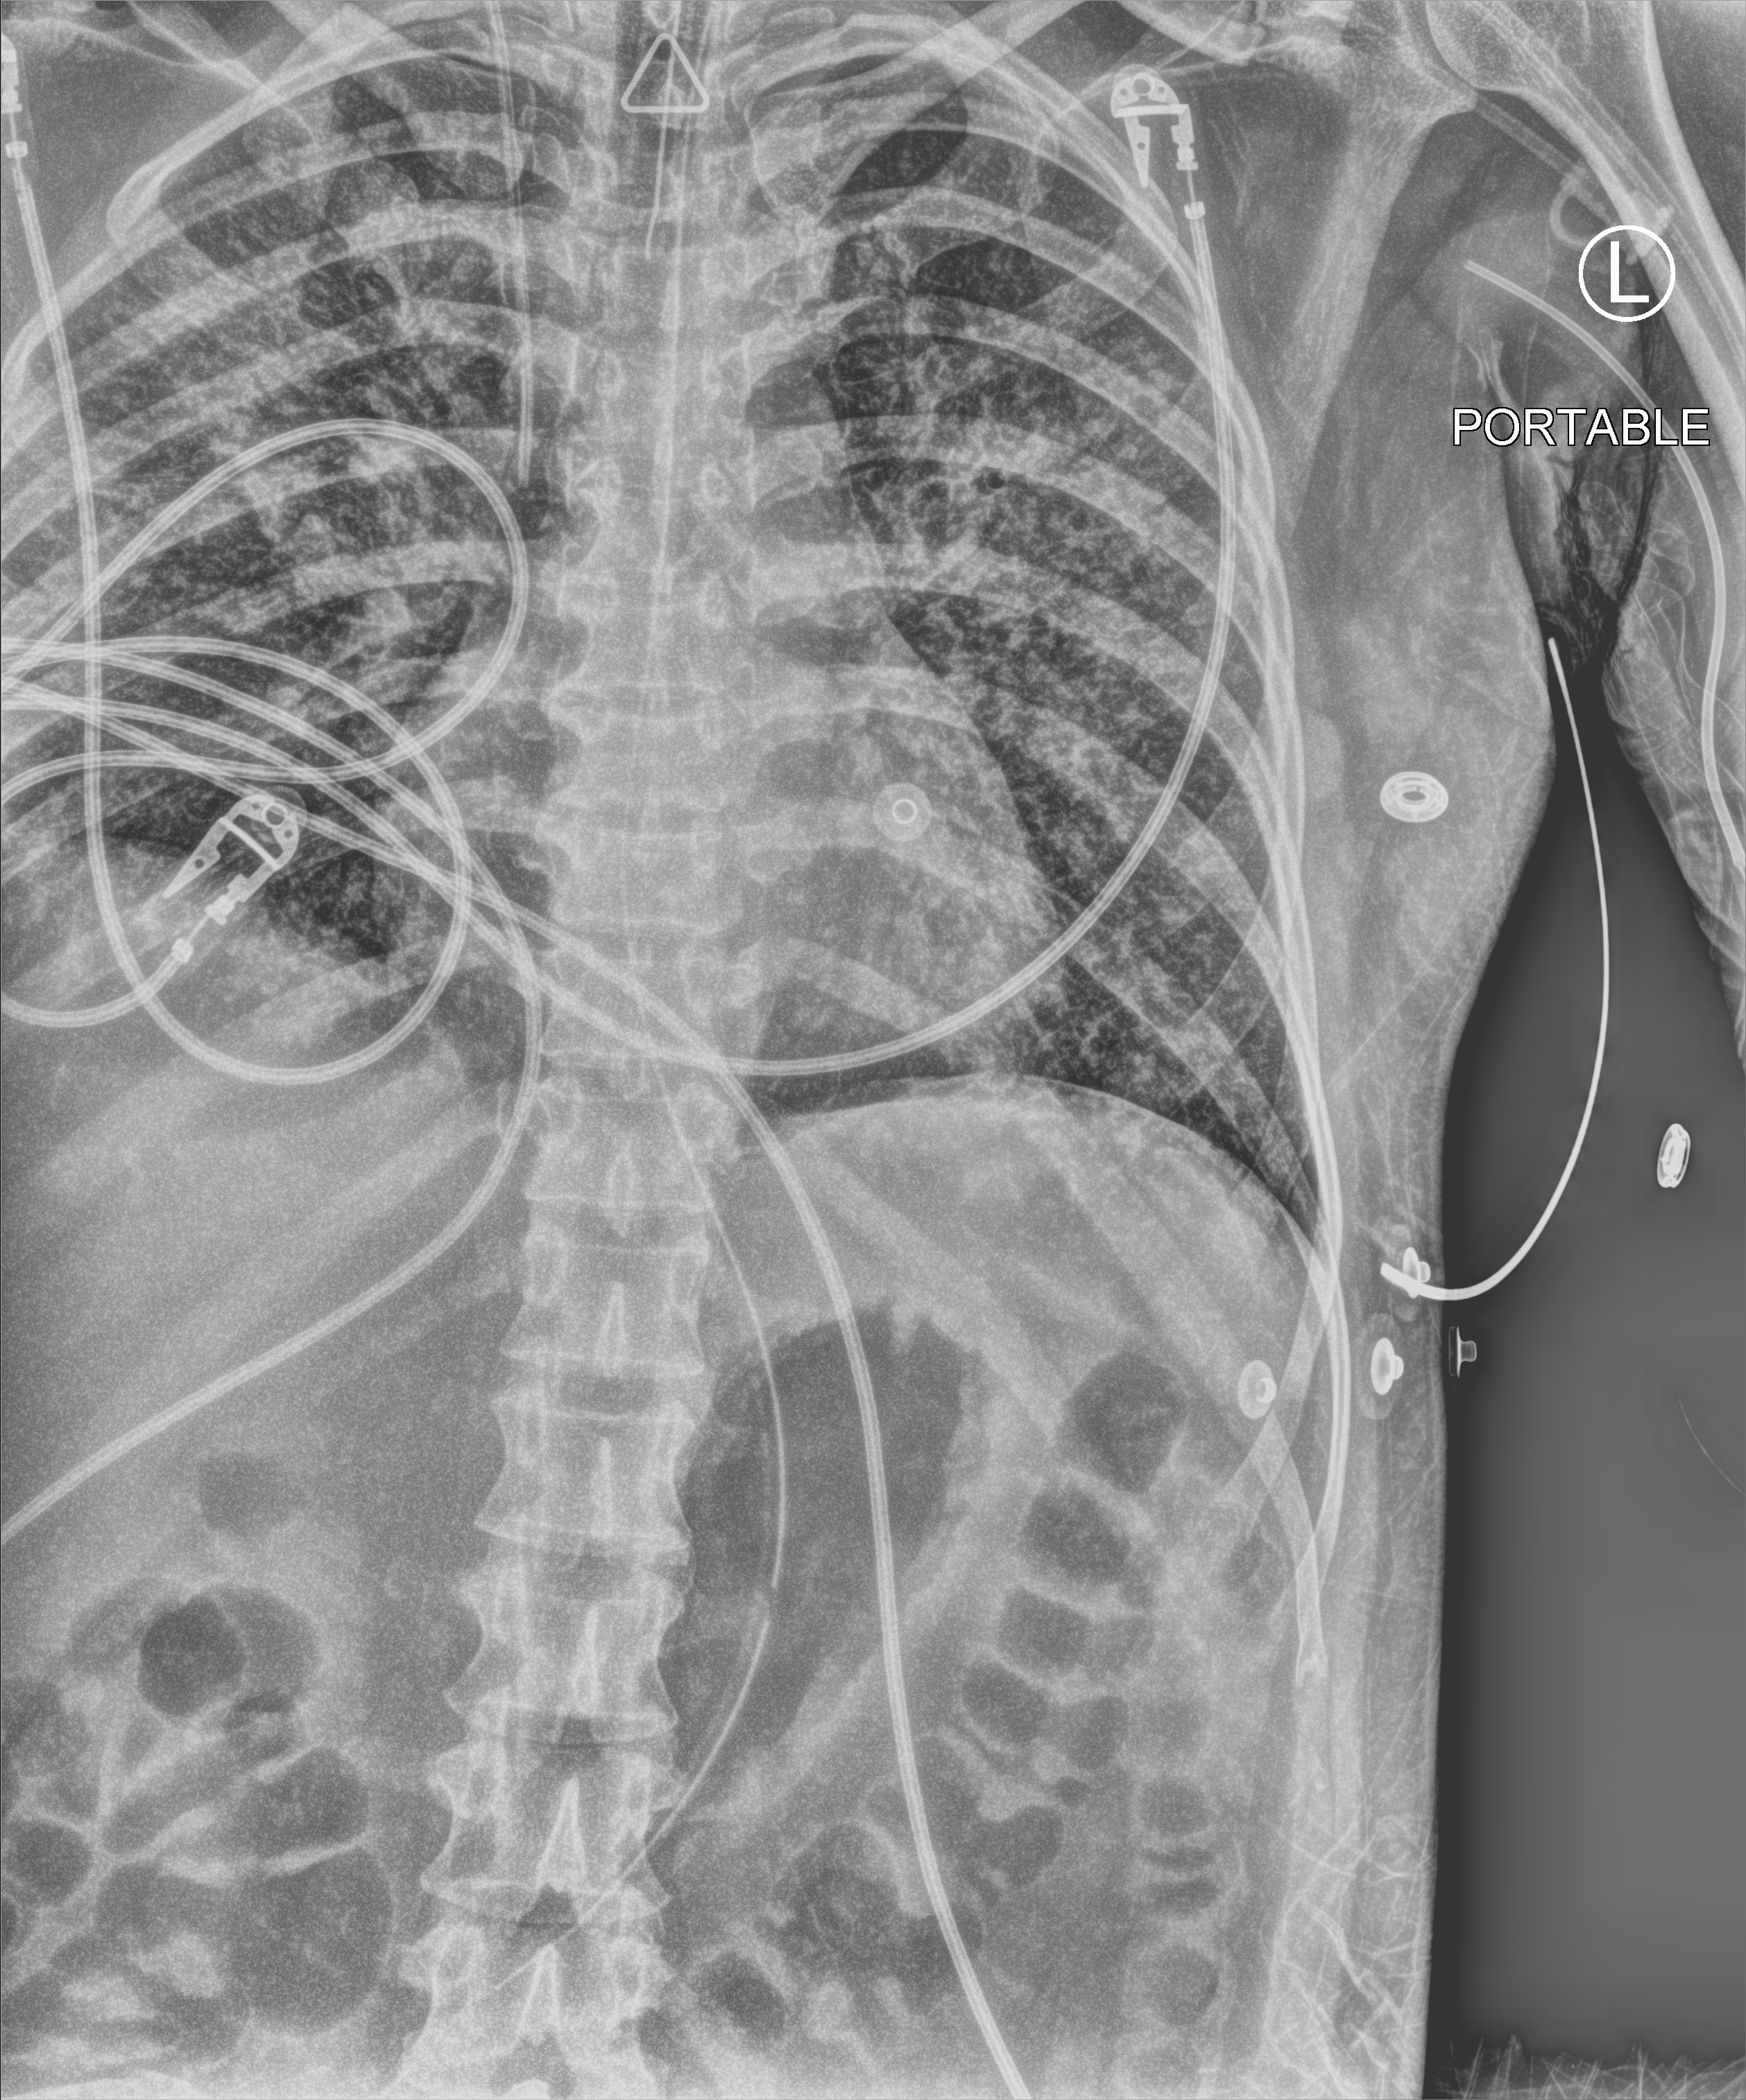
Bedside chest radiograph (computed radiography); anteroposterior (AP) projection. Female patient hospitalised with COVID-19, age 18–59 years.
From the hospital-stay record, not from the radiograph (when in the stay this image was taken is not recorded):
- diabetes (admission record): no
- length of hospital stay: 71 days